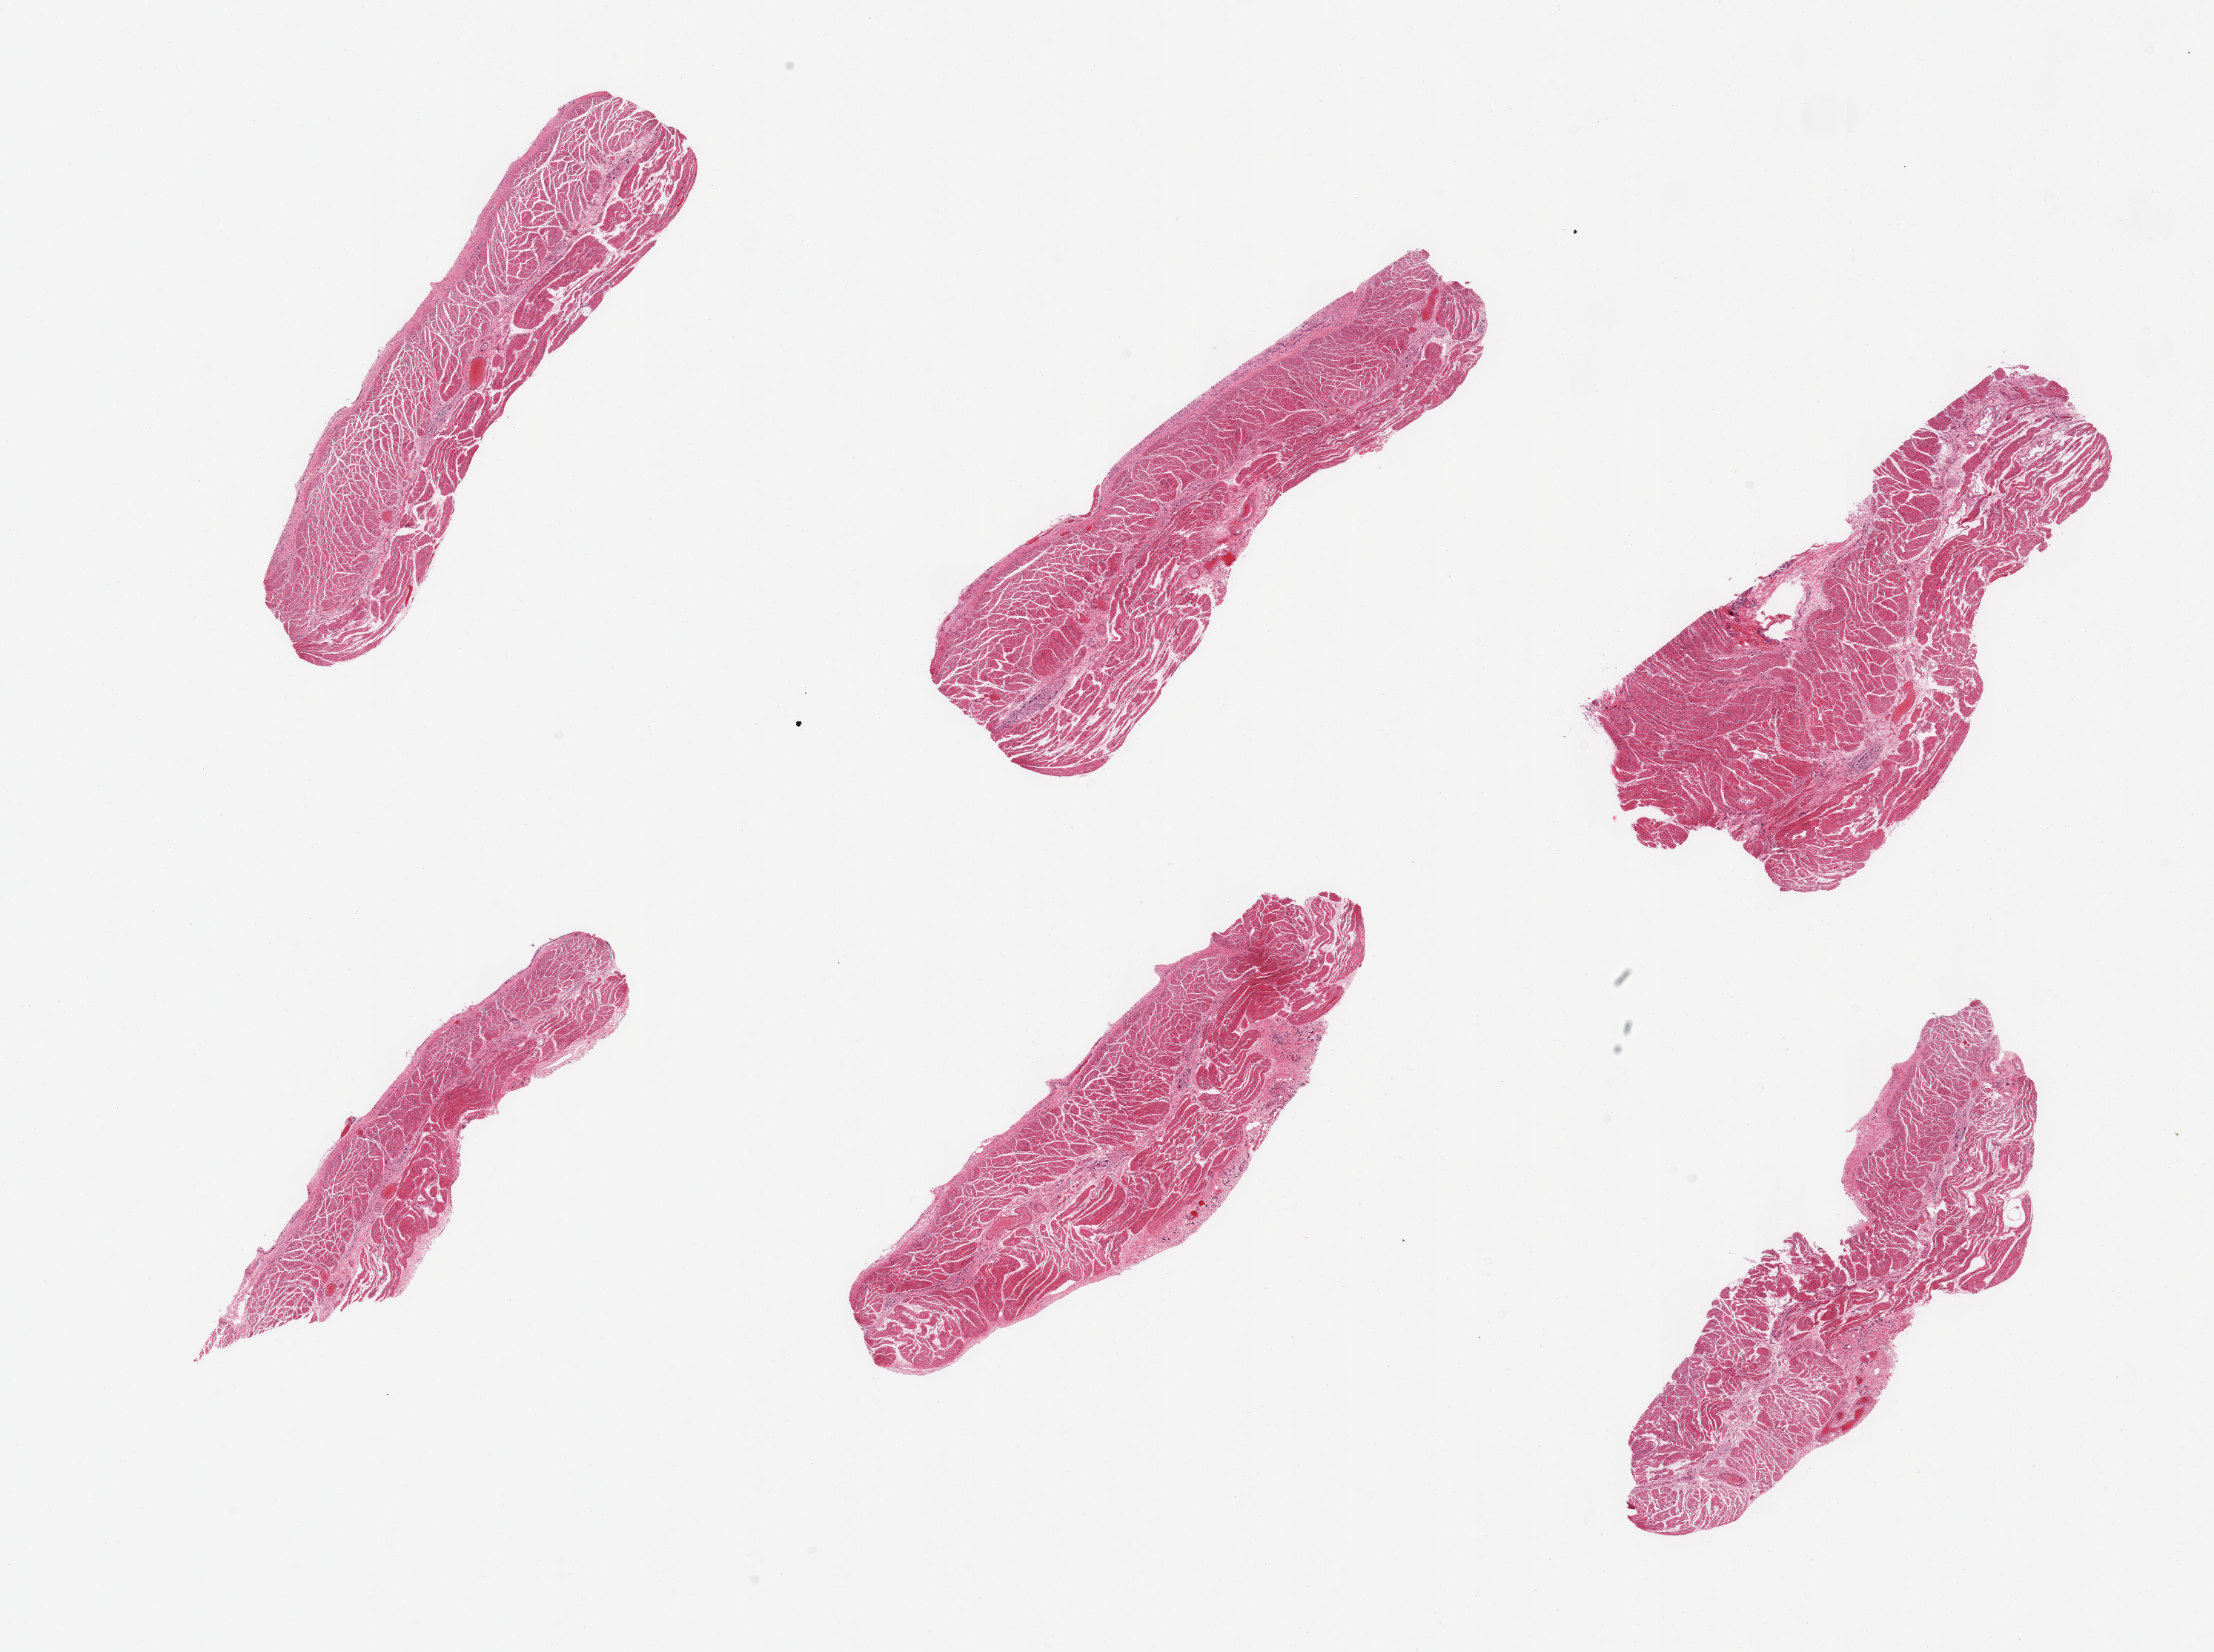
Whole-slide image, hematoxylin and eosin (H&E) stain — a low-resolution overview of the entire scanned area, about 23.6 x 17.6 mm (from a 20x scan); PAXgene-fixed paraffin-embedded (PFPE) section; target tissue: esophageal muscle; tissue donor sample. Donor sex: female.
* review note (as recorded): 6 pieces; well dissected